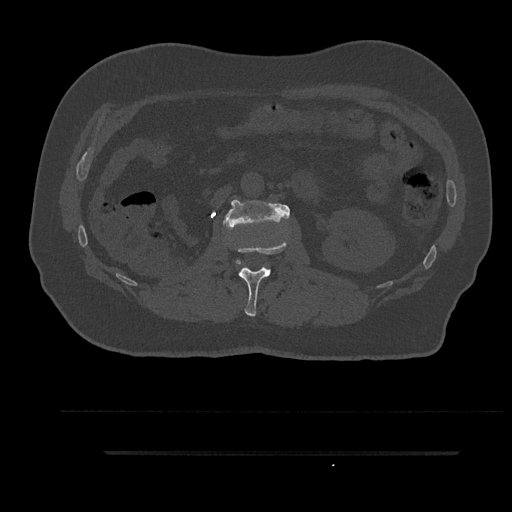
CT including the spine, one axial slice. Slice 149 of 797 in the series (ordered by position). Reconstruction kernel Br40s/3. Bone window (W 1800 / L 400 HU). 0.5 mm slice thickness. 512 × 512 image matrix, field of view 432 × 432 mm. Patient: male, 63 years. Case-level facts recorded for this patient, not image findings: primary cancer: renal.
Structures marked on this image (semi-automatic segmentation, software-assisted and operator-edited):
- L1 vertebra: bounding box <237,242,287,317> (left, top, right, bottom; pixels)
- L2 vertebra: <224,199,290,265>